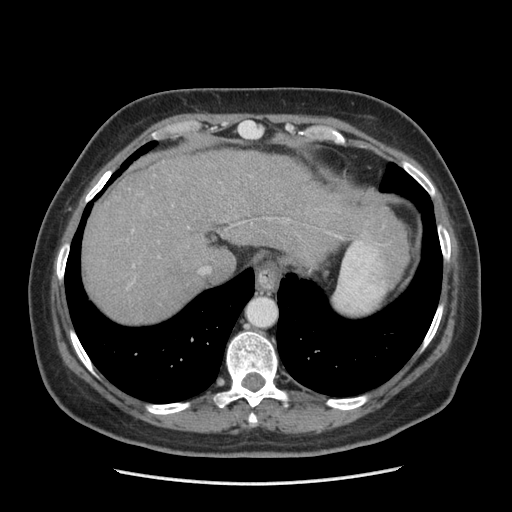
Contrast-enhanced abdominal CT (liver protocol), one axial slice; slice 167 of 185 in the series (ordered by position); reconstruction kernel STANDARD; soft-tissue window (W 400 / L 40 HU); 2.5 mm slice thickness; 512 × 512 image matrix, field of view 360 × 360 mm. From the clinical record (not read from this slice): diagnosis: hepatocellular carcinoma (patient treated with transarterial chemoembolisation; whether this scan precedes or follows treatment is not stated here); TNM stage (as recorded): Stage-I; Child-Pugh class: A; tumour differentiation: poorly differentiated.
Annotated regions visible in this slice (semi-automatic segmentation, software-assisted and operator-edited):
- abdominal aorta: bounding box [x1, y1, x2, y2] px = [247, 297, 276, 327]
- liver parenchyma outside the tumour (the mass and vessels are separate outlines, so this box may not span the whole liver): [82, 149, 408, 322]